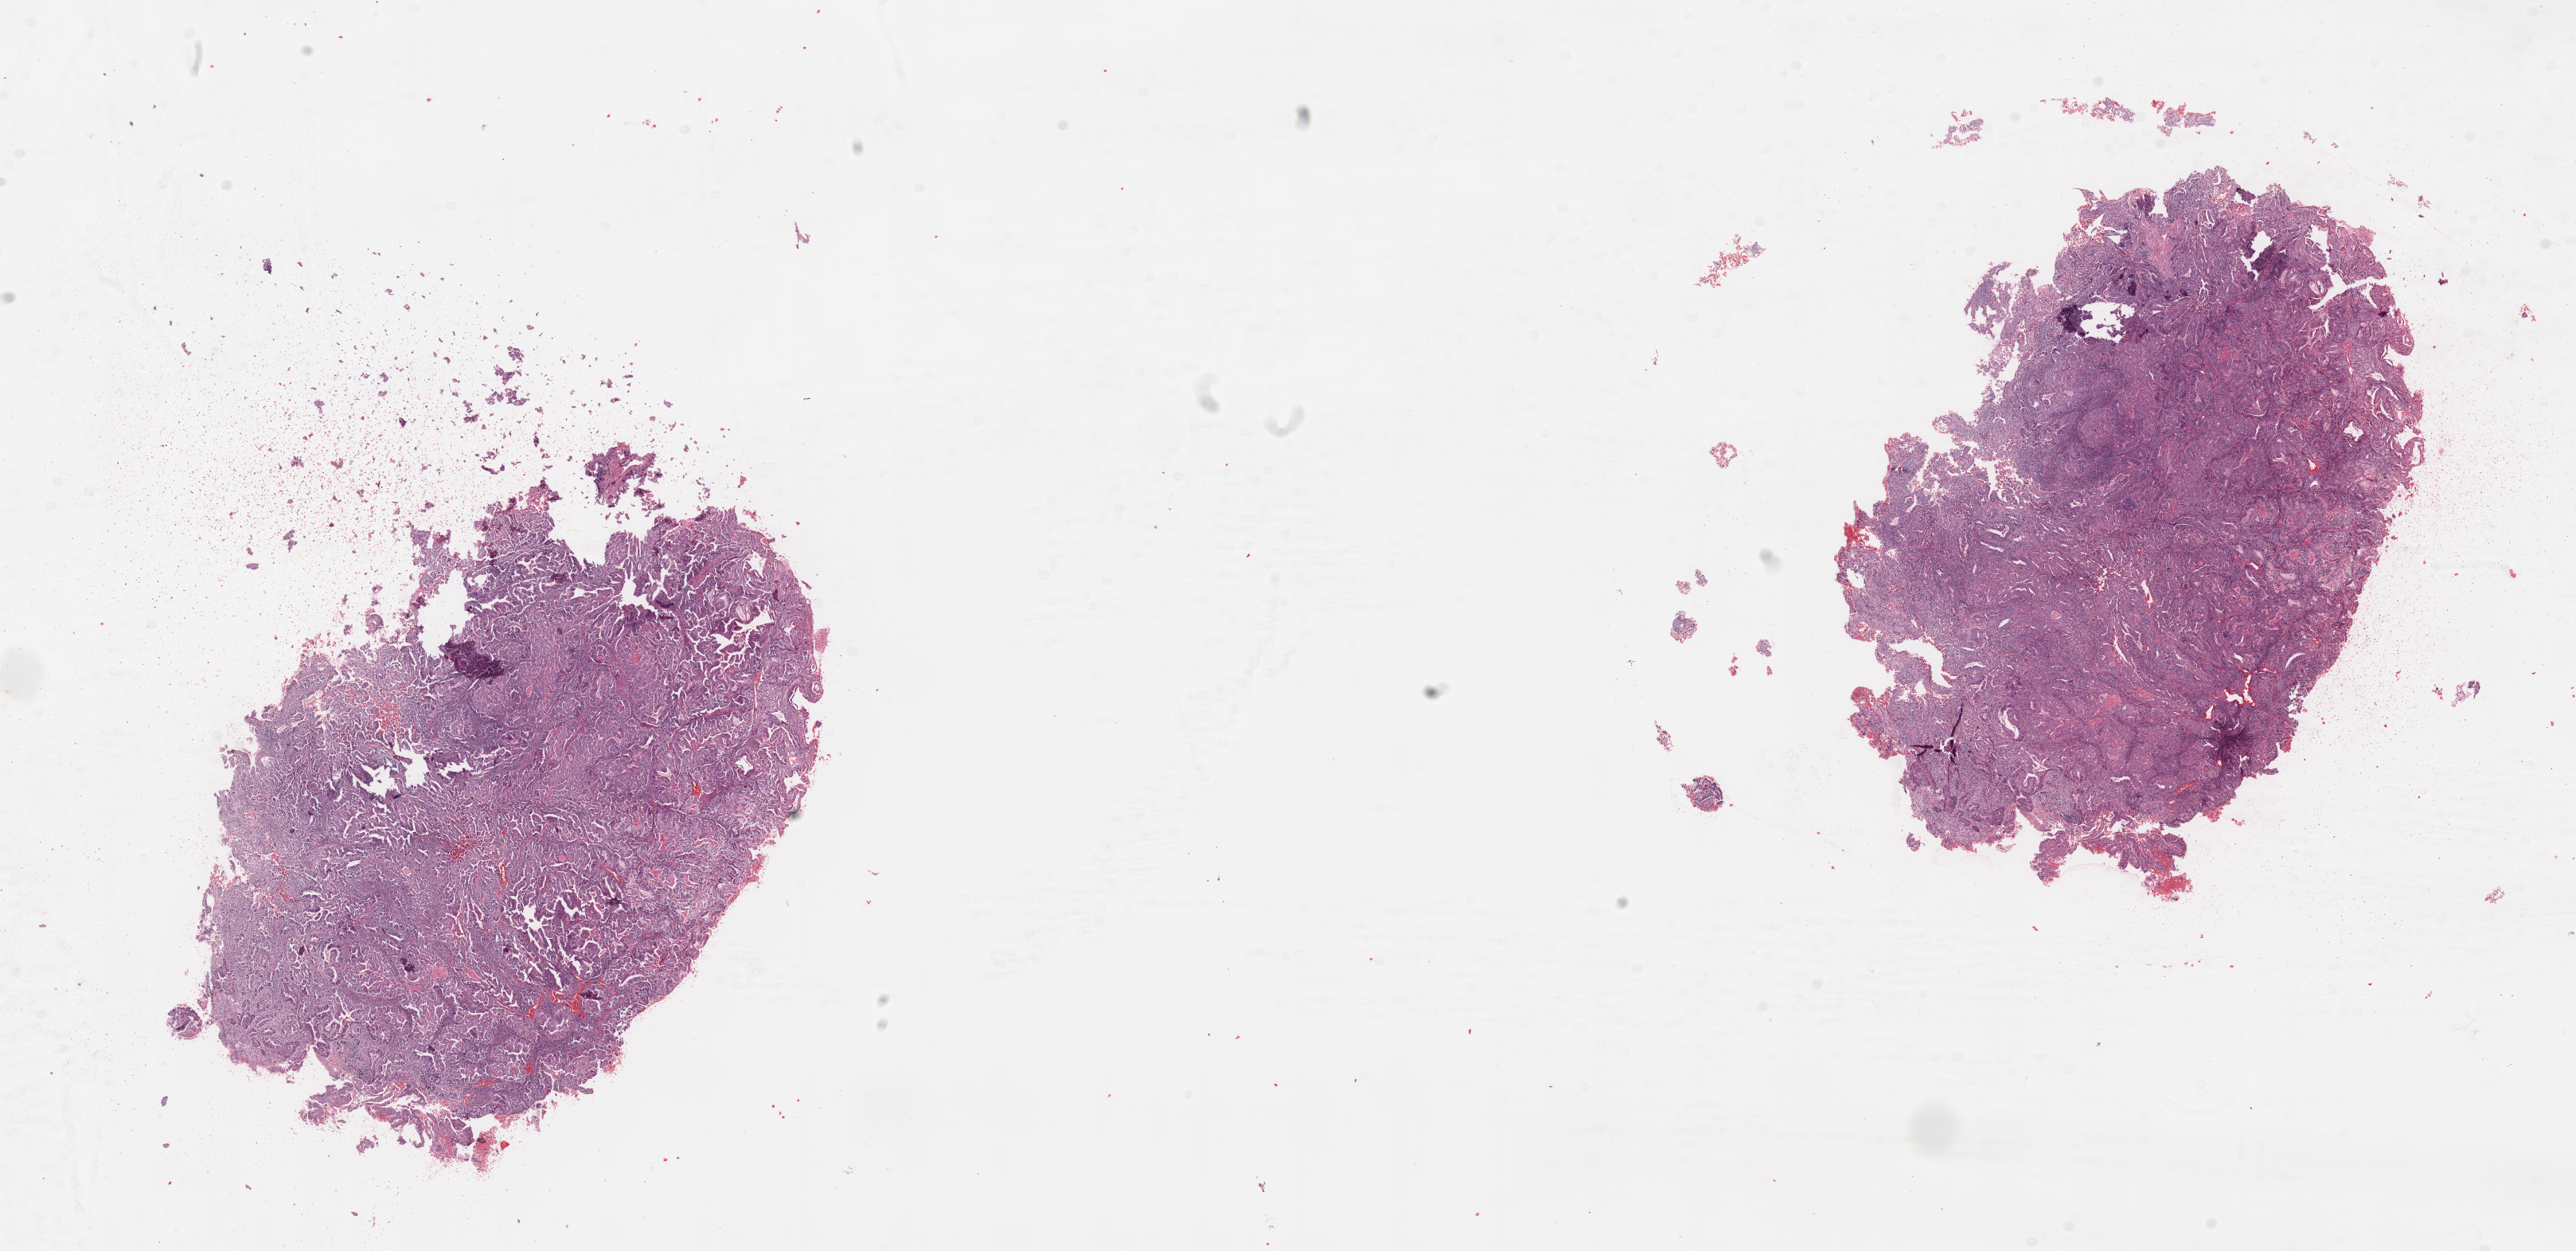
H&E whole-slide image — whole scanned area (about 25.6 x 12.4 mm) shown as a low-resolution overview; tumour tissue sample, sampled site: uterus. 51-year-old female patient. Histologic grade: G2 (moderately differentiated). Pathologist review of this section (percent, as recorded): tumour nuclei 90%, necrosis 2%.
- AJCC pathologic stage: I
- diagnosis: Endometrioid adenocarcinoma, NOS